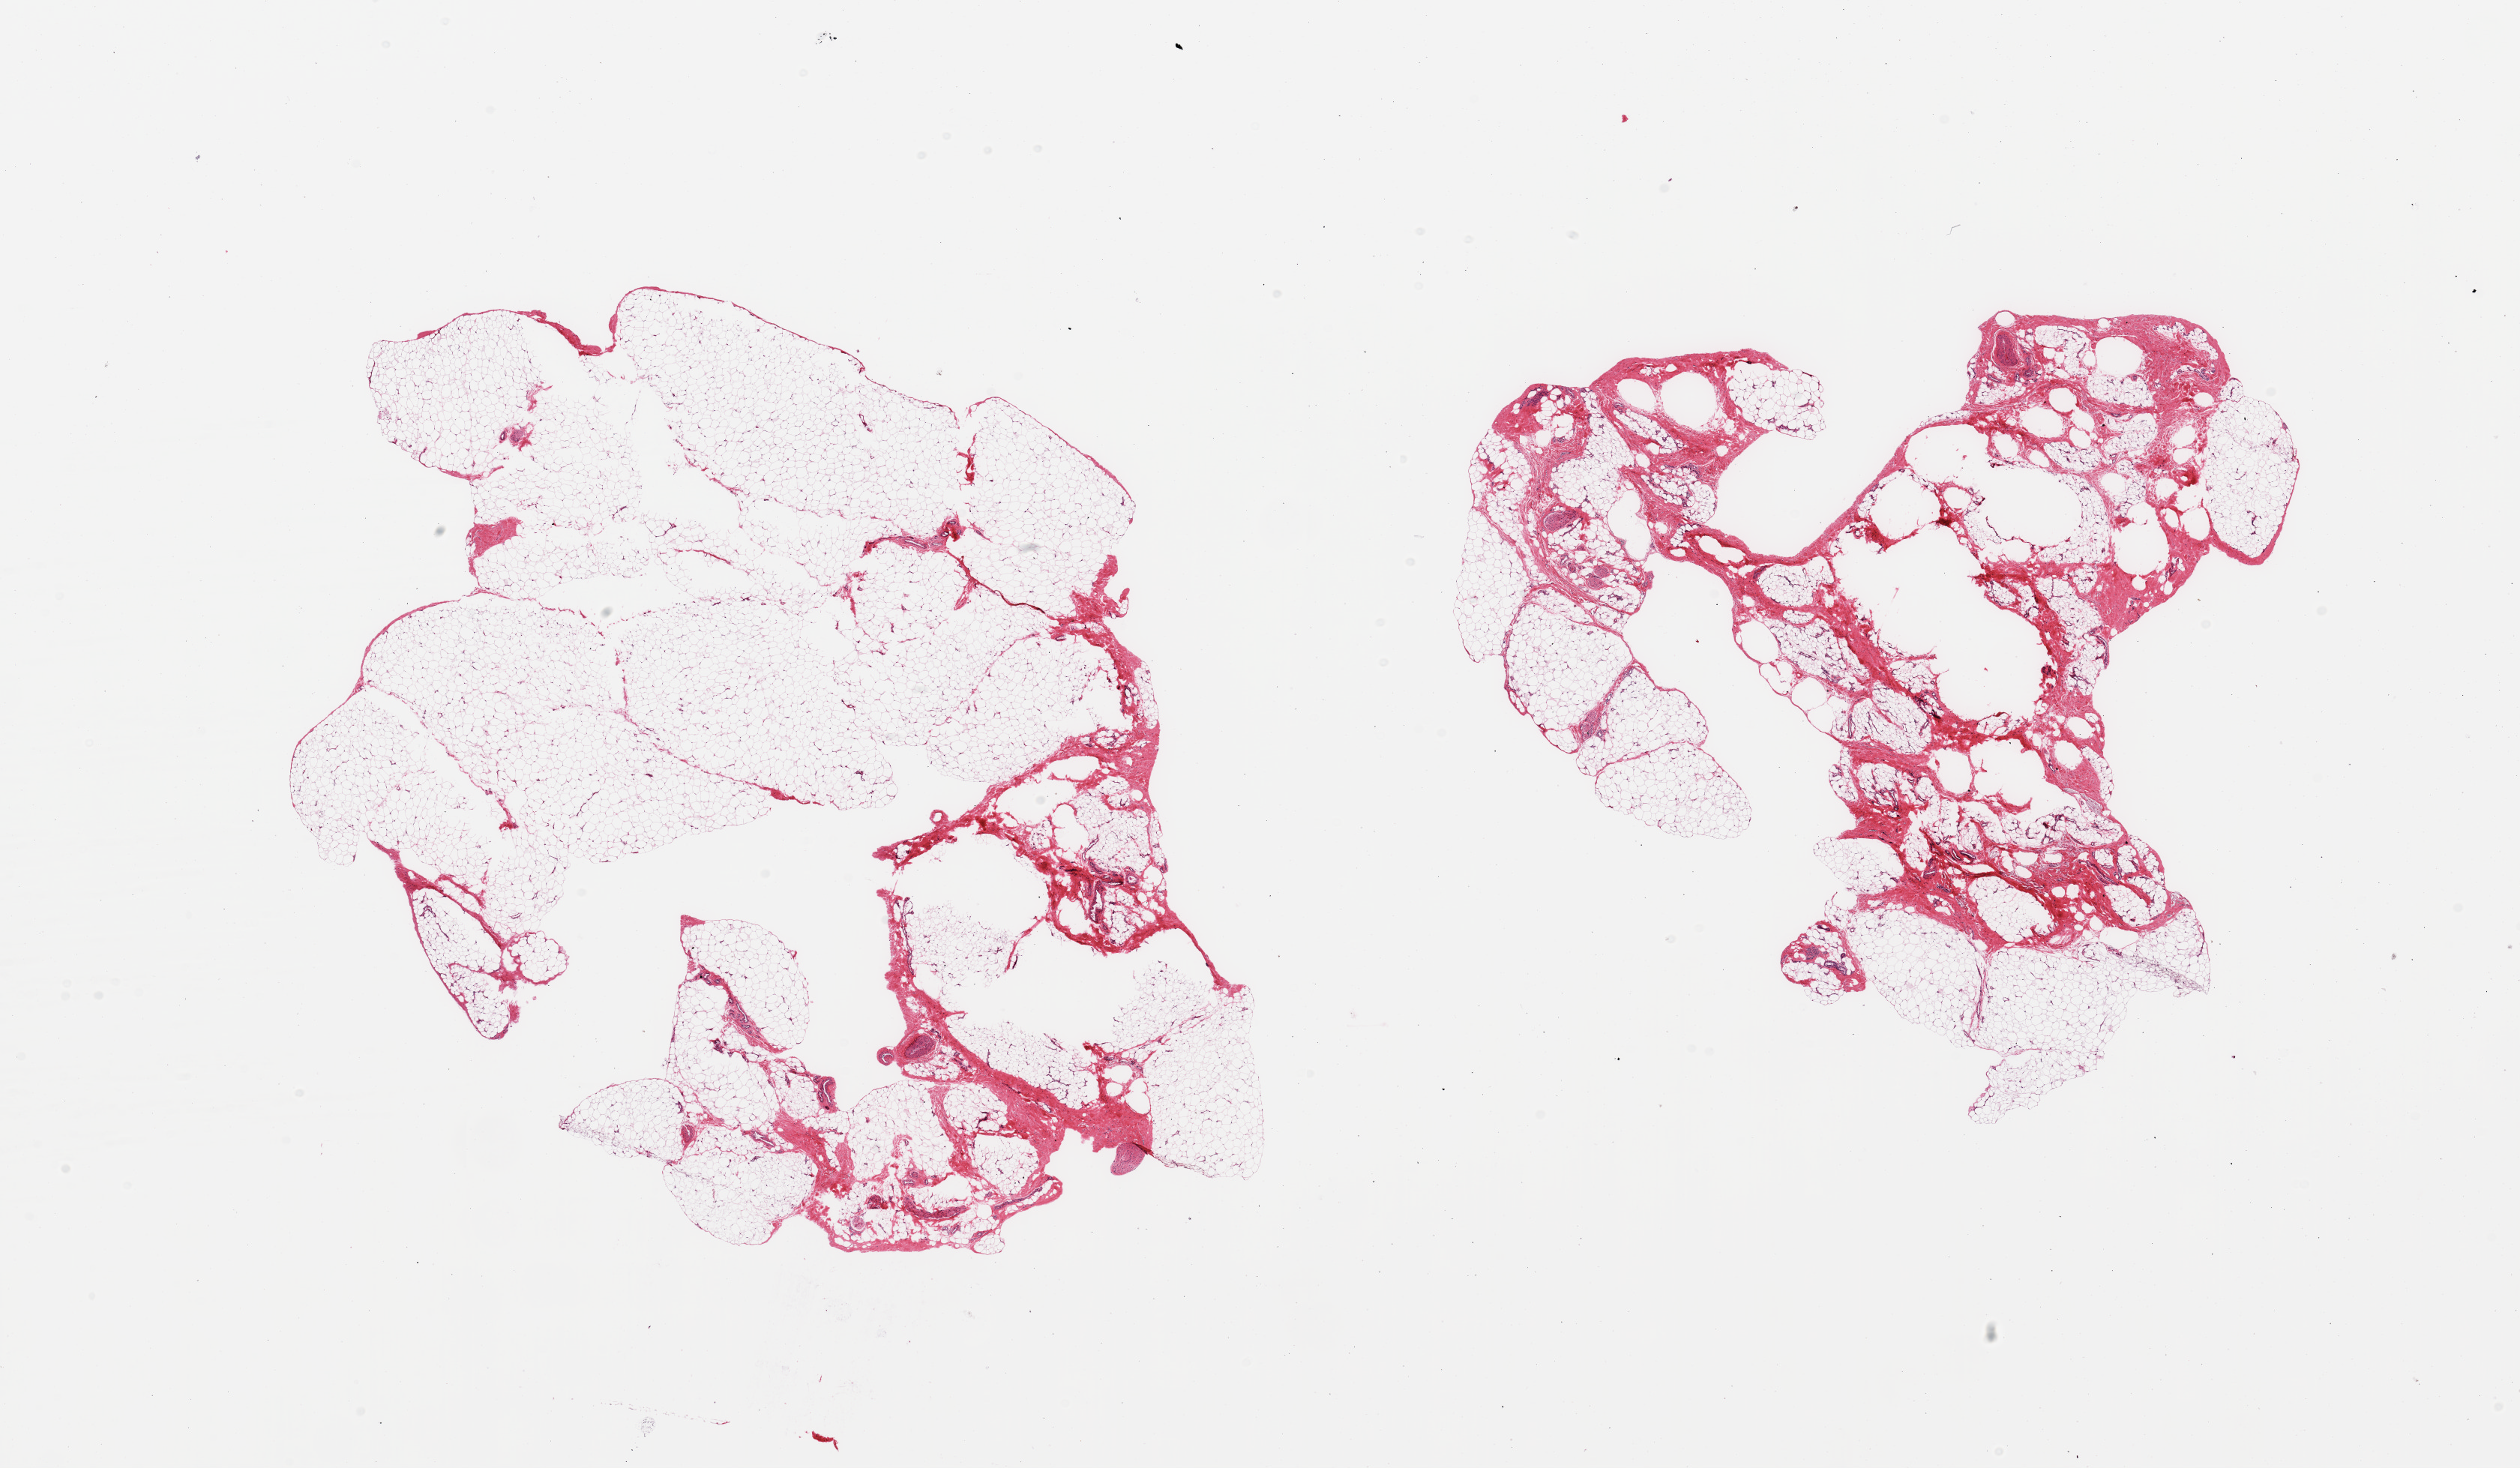
Digitized hematoxylin and eosin (H&E)-stained section — a low-resolution overview of the entire scanned area, about 26.6 x 15.5 mm, PAXgene-fixed, paraffin-embedded tissue, target tissue: adipose tissue, tissue donor sample. Donor sex: male.
Pathologist's review note for this sample: 2 pieces; 5 & 20% fibrous content.